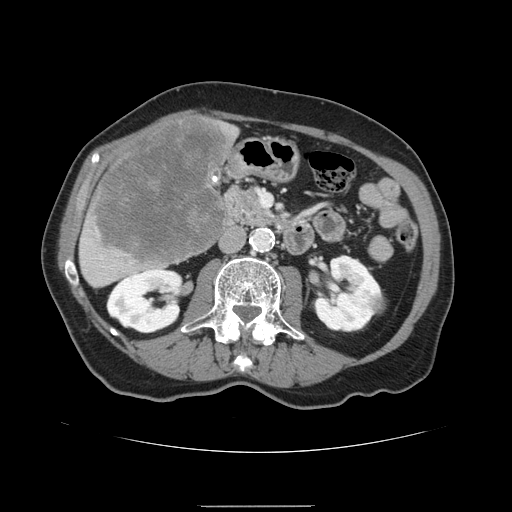
Contrast-enhanced abdominal CT, one axial slice. Position 54 of 168 along the scan axis. 120 kVp. Soft-tissue window (W 400 / L 40 HU). 2.5 mm slice thickness. 512 × 512 image matrix, field of view 386 × 386 mm. Male patient, age 74 years. Case-level facts recorded for this patient, not image findings: diagnosis: colorectal cancer liver metastases, imaged before liver resection.
Outlined on this slice (expert manual segmentation):
- liver: box from (x=78, y=114) to (x=239, y=288) px
- liver metastasis: (x=90, y=117)–(x=230, y=266)